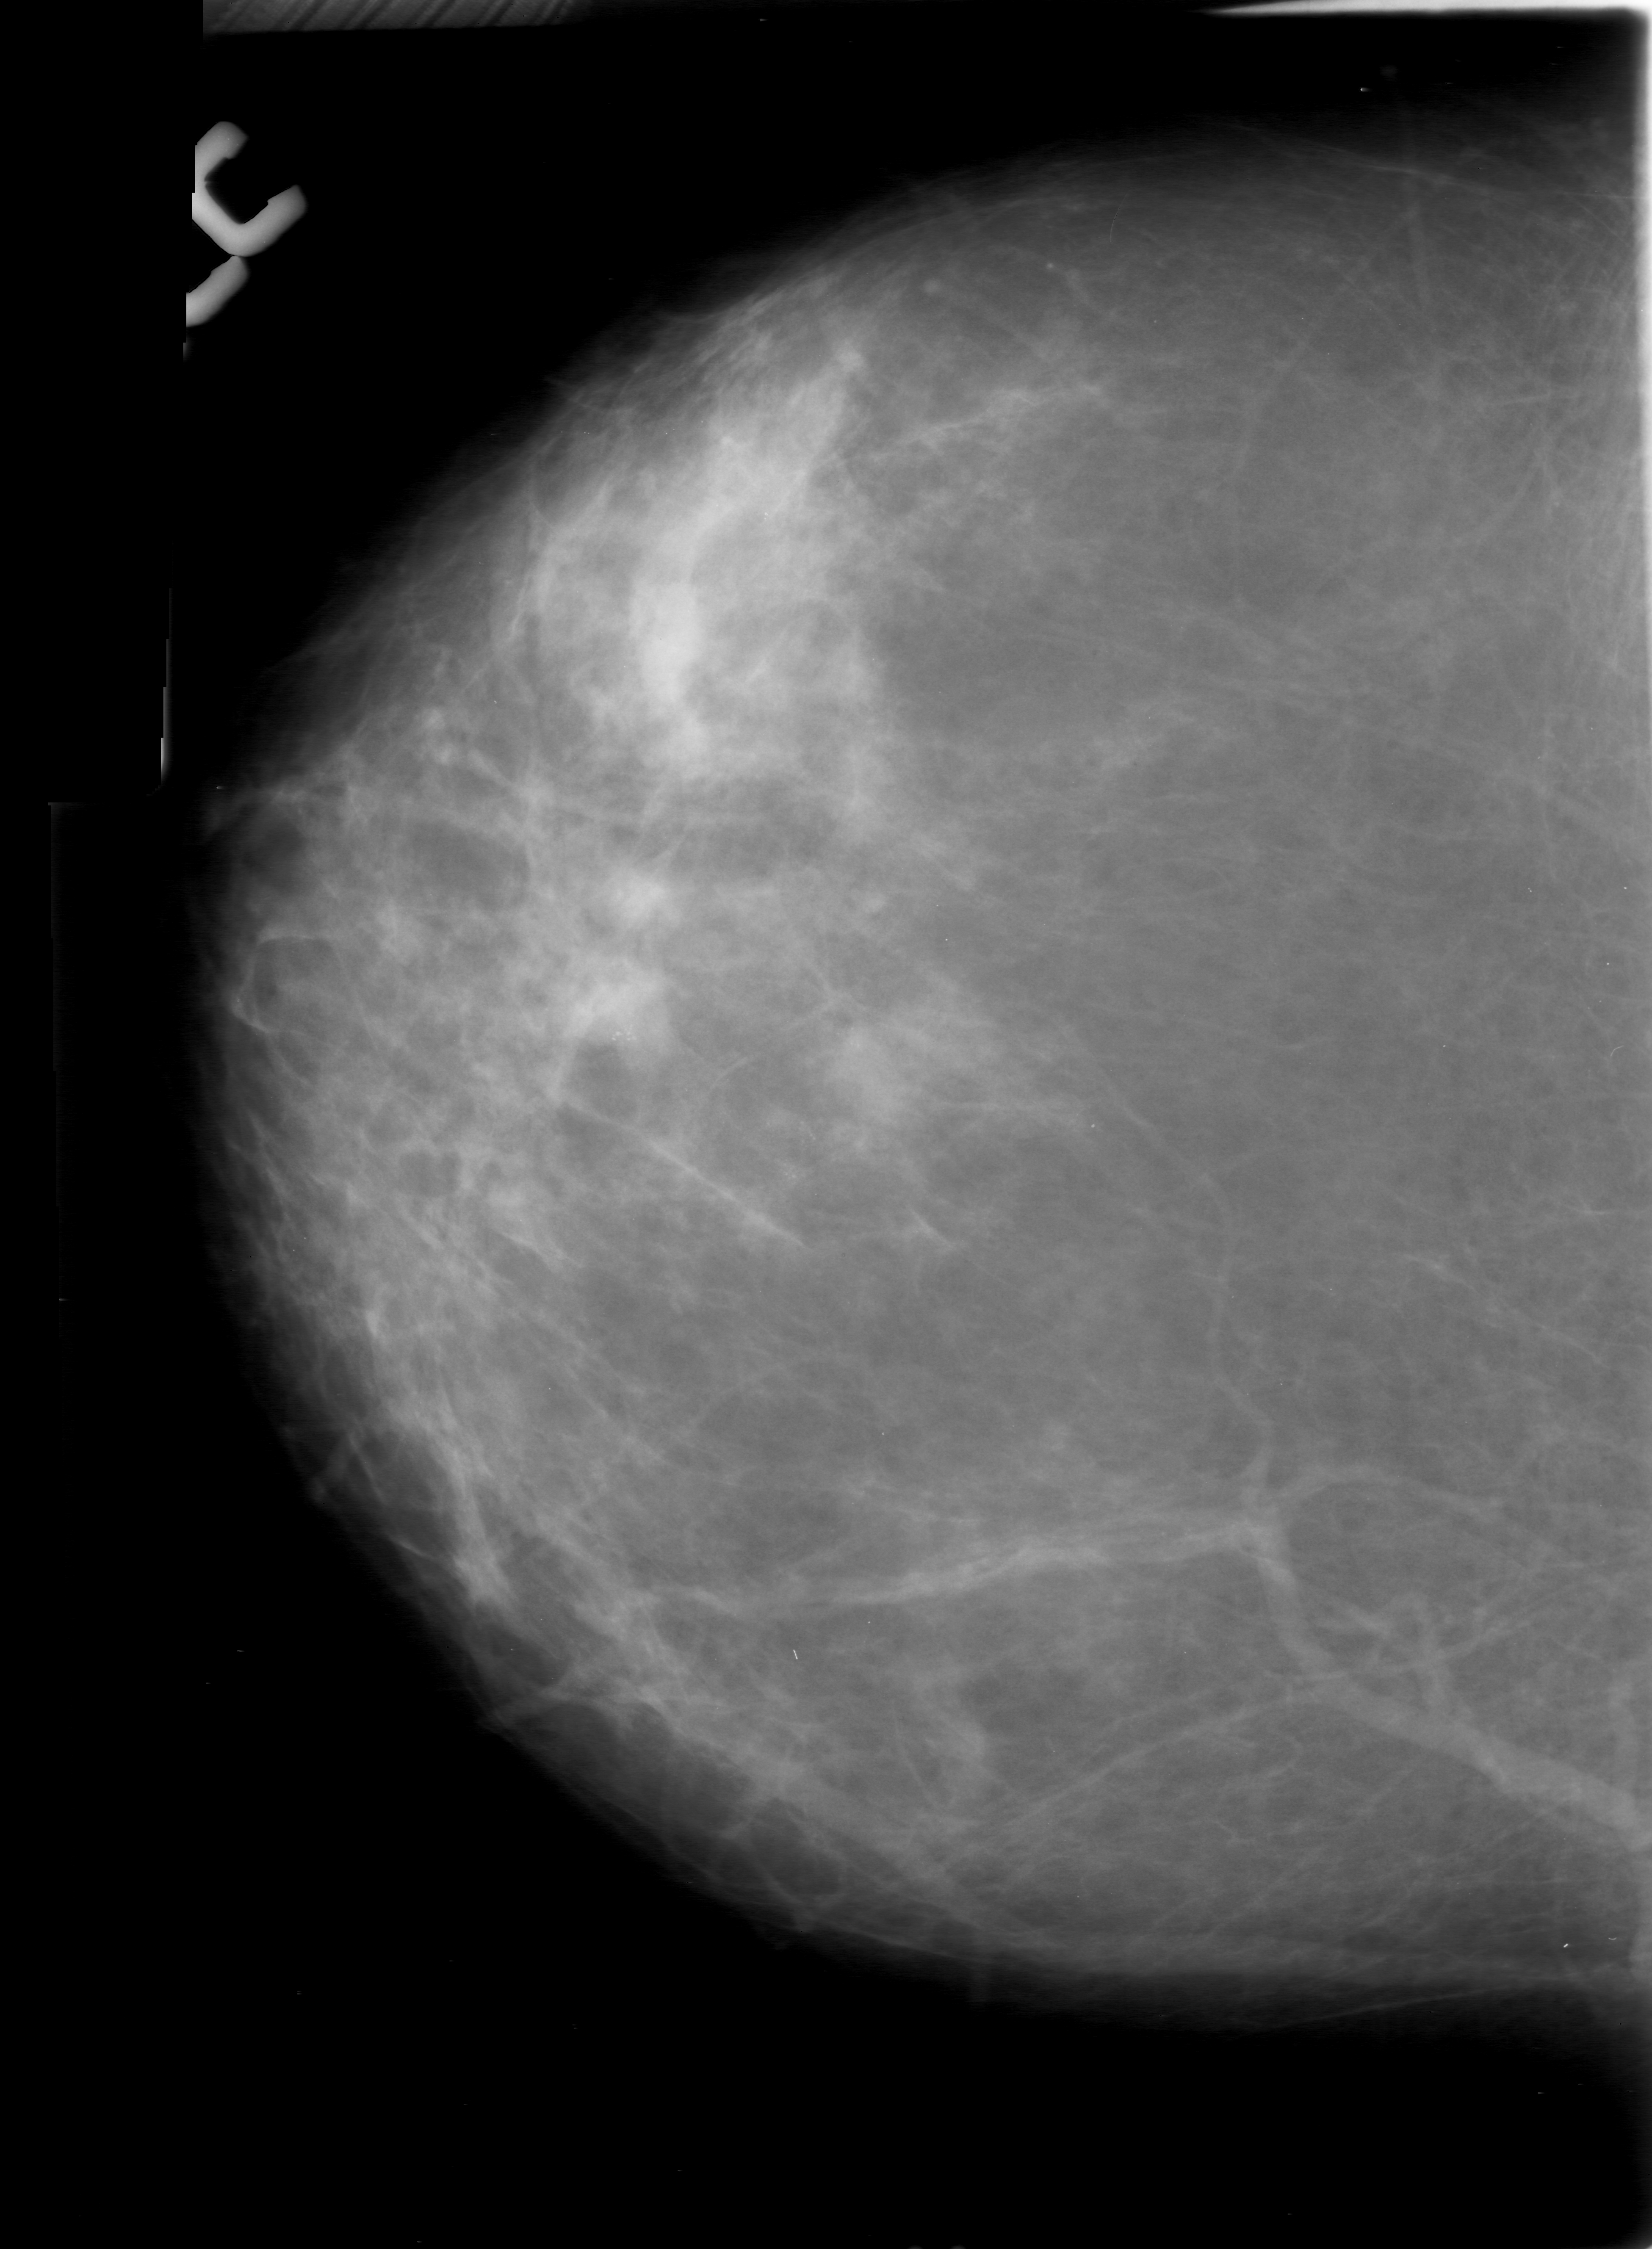
Mammogram (digitized film); right breast; CC view; 1652 × 2249 image matrix.
Marked abnormalities (boxes around the expert regions of interest):
- calcifications, morphology pleomorphic, distribution clustered; BI-RADS assessment category 0; pathology result (as recorded, not read from the image): malignant: box from (x=479, y=912) to (x=1053, y=1284) px